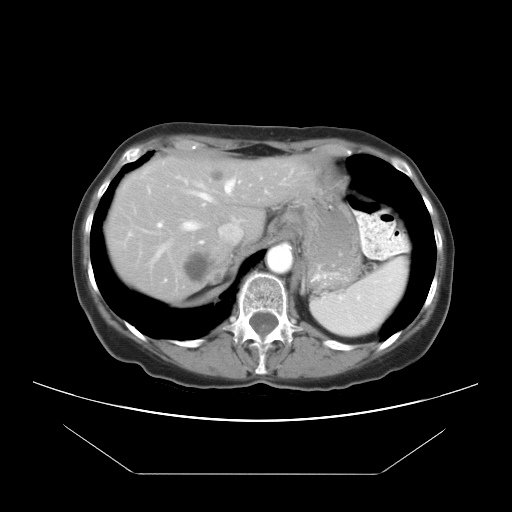
Contrast-enhanced abdominal CT, one axial slice. Position 17 of 21 along the scan axis. 120 kVp. Intravenous contrast given. Soft-tissue window (W 400 / L 40 HU). 7.5 mm slice thickness. 512 × 512 image matrix, field of view 392 × 392 mm. Female patient, age 72 years. From the clinical record (not read from this slice): diagnosis: colorectal cancer liver metastases, imaged before liver resection; multiple liver metastases: yes; largest metastasis: 4 cm; chemotherapy before resection: yes.
Outlined on this slice (expert manual segmentation):
- hepatic veins: bounding box (x1, y1, x2, y2) in pixels: (158, 179, 235, 255)
- liver: (107, 158, 303, 298)
- planned liver remnant (the part of the liver to remain after resection): (107, 158, 303, 271)
- portal vein (with intrahepatic branches): (157, 223, 162, 228)
- liver metastasis: (207, 168, 224, 182)
- liver metastasis: (182, 251, 218, 286)